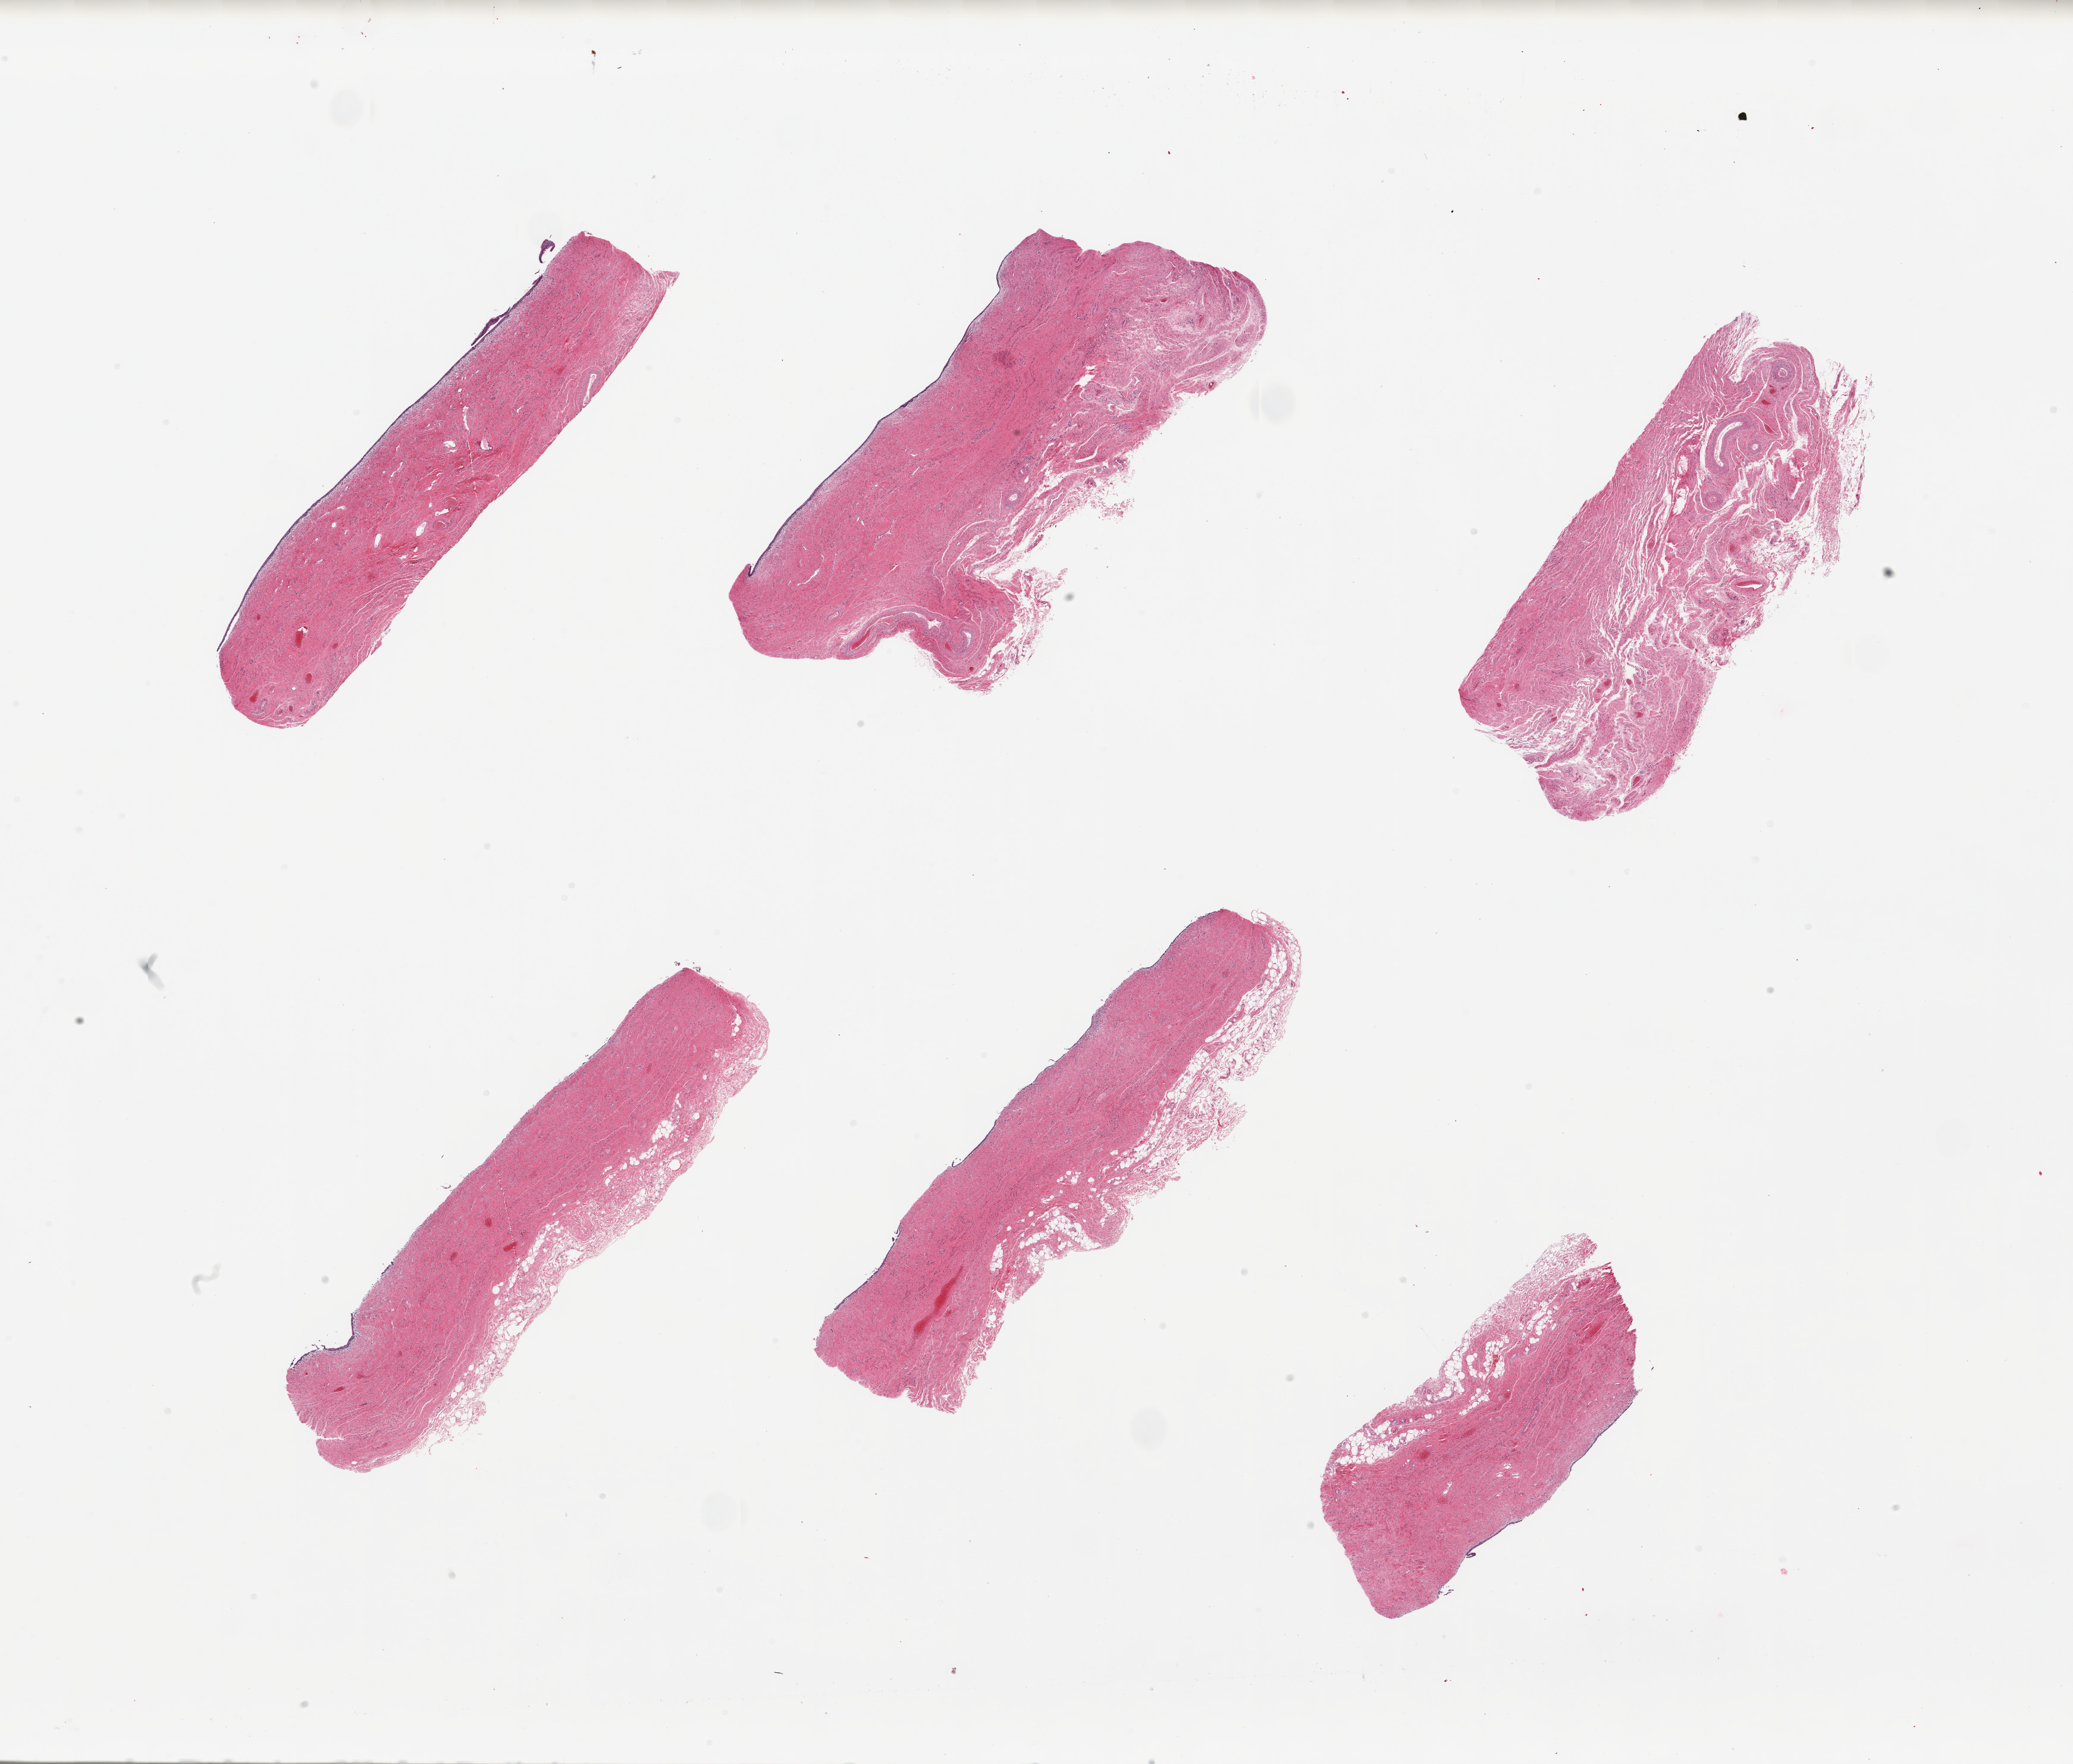
Haematoxylin and eosin whole-slide image, brightfield — a low-resolution overview of the entire scanned area, about 27.6 x 23.5 mm. PAXgene-fixed, paraffin-embedded tissue. Target tissue: vagina. Tissue donor sample. Donor: female.
Reviewer comment on this tissue sample: 6 pieces, sloughing squamous mucosa.